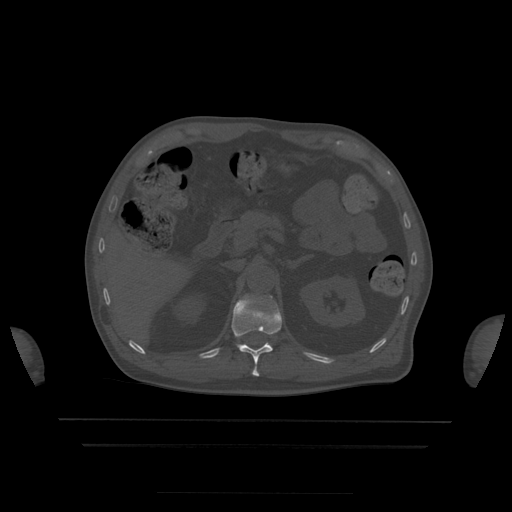
CT including the spine, one axial slice; position 191 of 522 along the scan axis; bone window (W 1800 / L 400 HU); 512 × 512 image matrix, field of view 436 × 436 mm. Patient age 68 years. Case-level facts recorded for this patient, not image findings: primary cancer: urothelial.
Annotated regions visible in this slice (semi-automatic segmentation, software-assisted and operator-edited):
- L1 vertebra: bounding box [x1, y1, x2, y2] px = [260, 296, 277, 305]
- T12 vertebra: [232, 298, 282, 377]